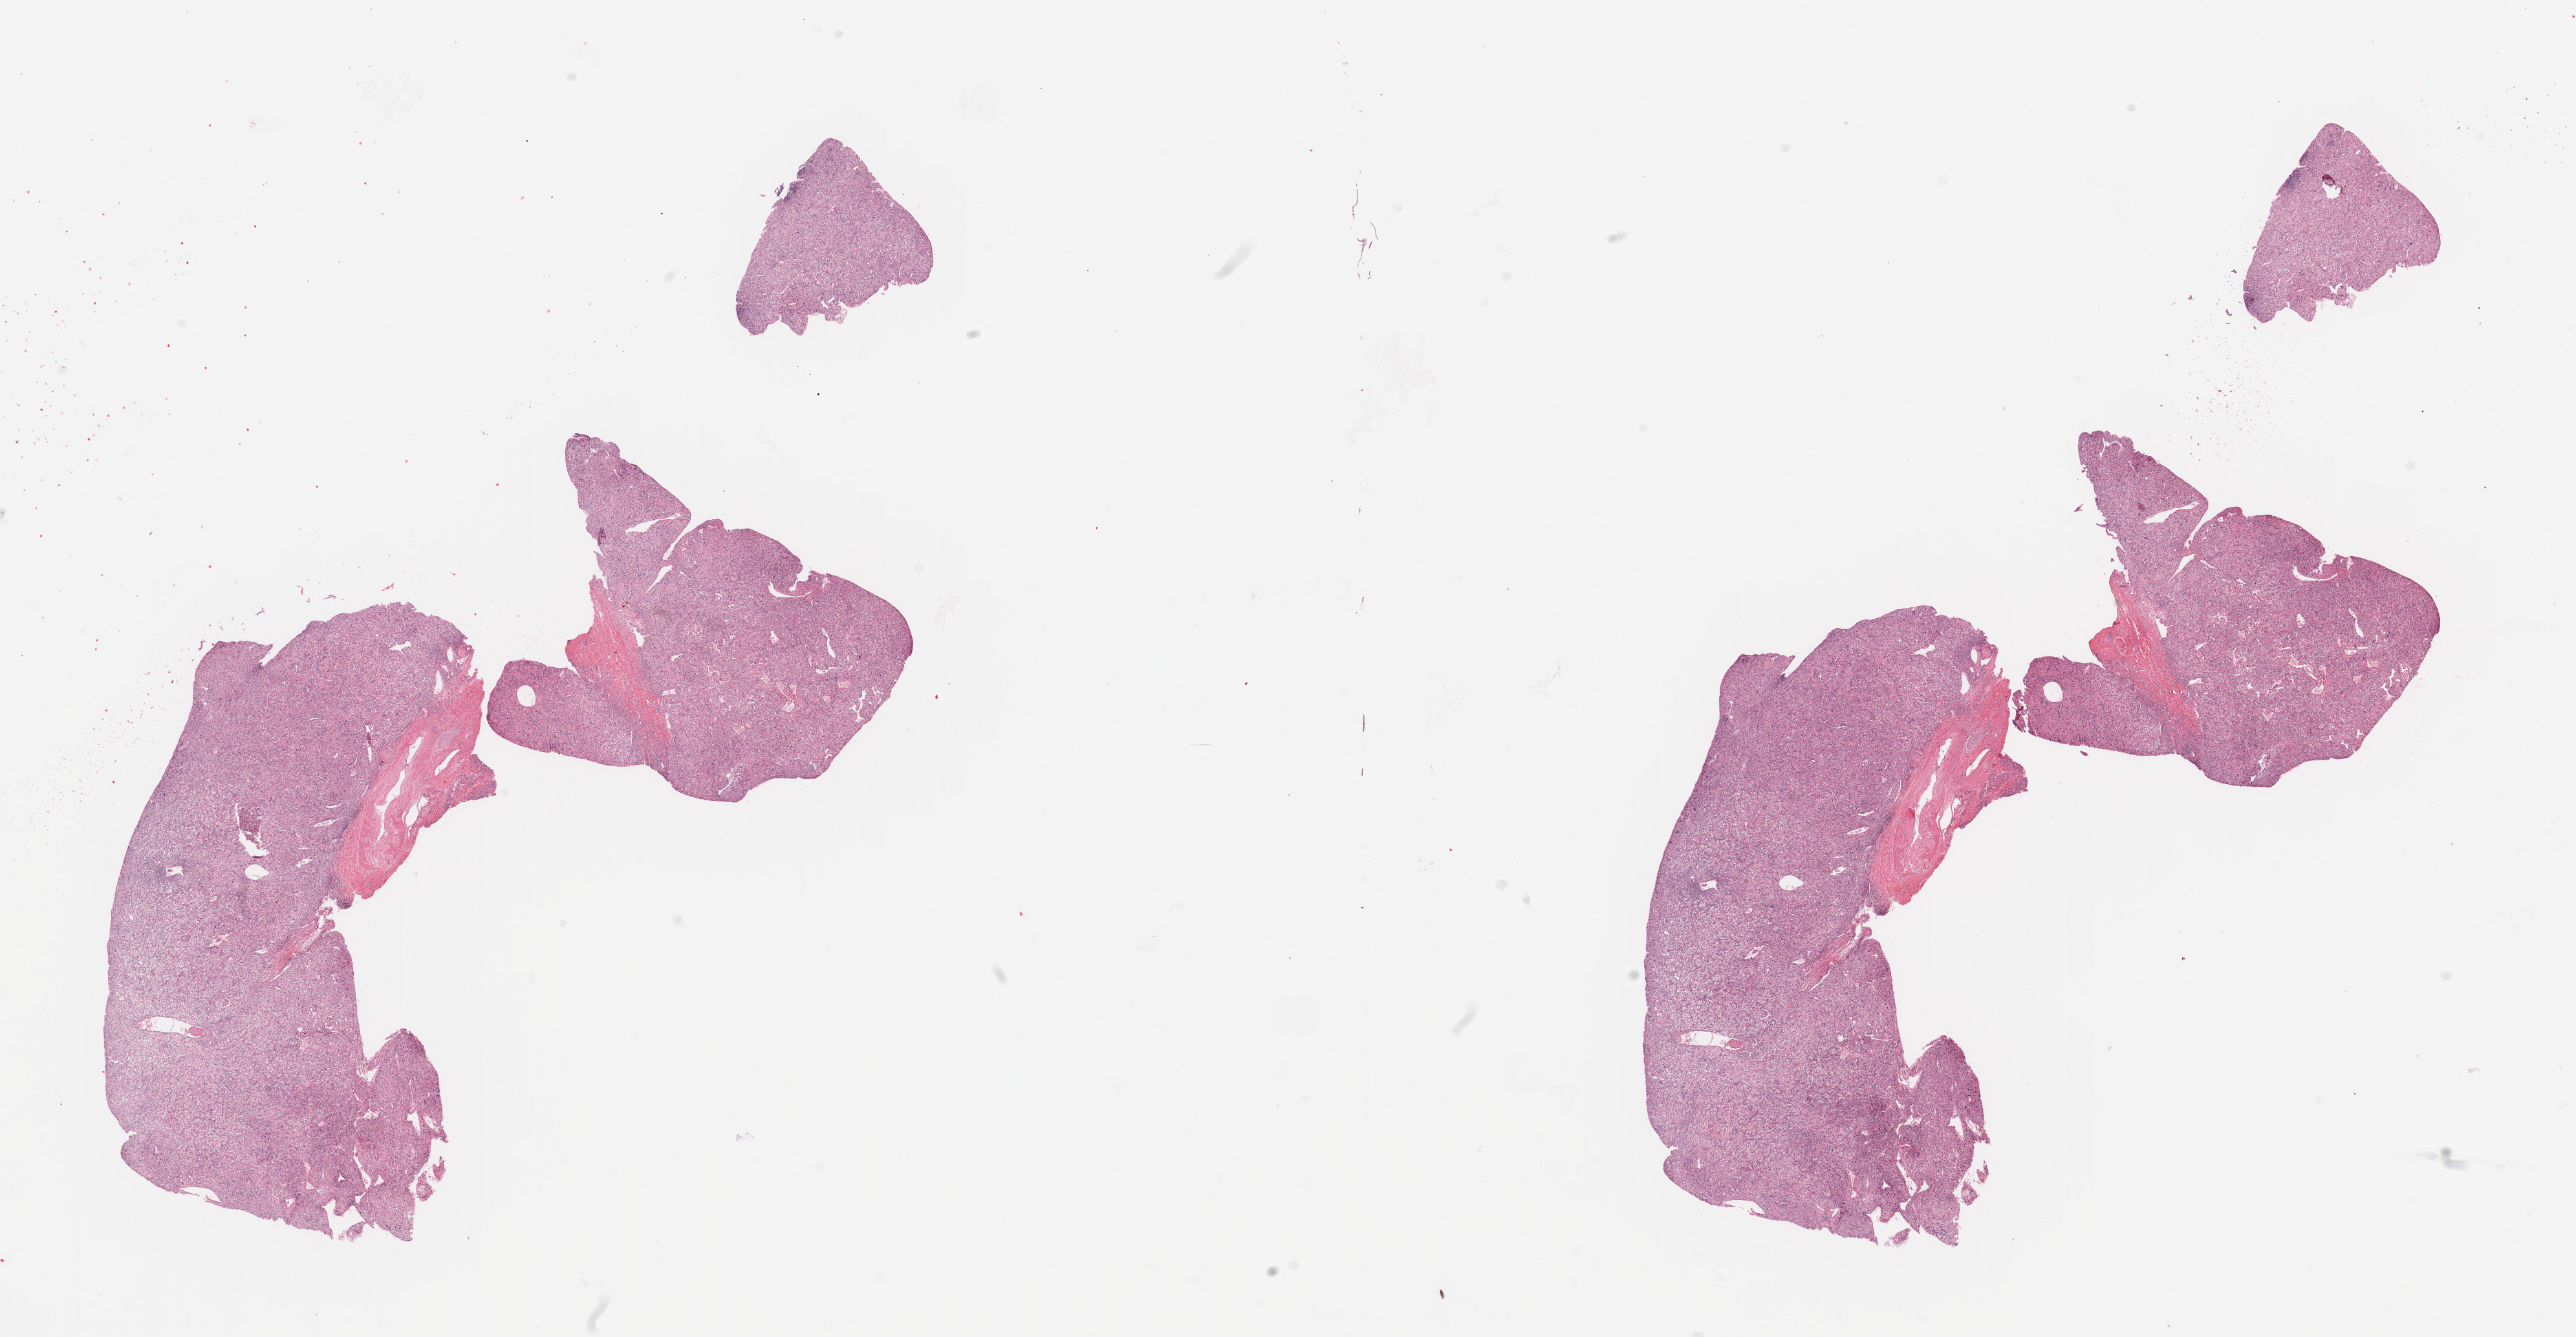
H&E whole-slide image, low-resolution overview of the scanned area, about 31.5 x 16.4 mm (slide scanned at 20x), tumour tissue sample, sampled site: kidney. 66-year-old female patient. Histologic grade: G4 (undifferentiated). Pathologist review of this section (percent, as recorded): tumour nuclei 90%, necrosis 2%.
• primary tumour site (as recorded): lower pole
• AJCC pathologic stage: III
• diagnosis: Renal cell carcinoma, NOS